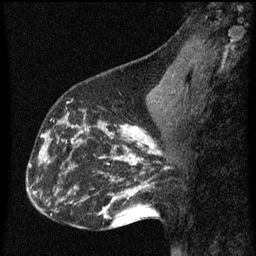
Breast MRI (dynamic contrast-enhanced), one sagittal slice. Slice 26 of 60 in the series (ordered by position). Dynamic contrast-enhanced series, image 2 of 3 at this slice position (ordered by acquisition). 1.5 T. TE 4.2 ms, TR 8 ms. 256 × 256 image matrix, field of view 180 × 180 mm. Female patient, age 43 years.
Structures marked on this image (semi-automatic segmentation, software-assisted and operator-edited):
- analysis volume of interest (the breast-tissue region the enhancement analysis was run in; not a lesion): bounding box (x1, y1, x2, y2) in pixels: (53, 104, 101, 155)
- tumour enhancement mask (voxels above the 70 % enhancement threshold inside the analysis volume of interest): (59, 116, 90, 147)